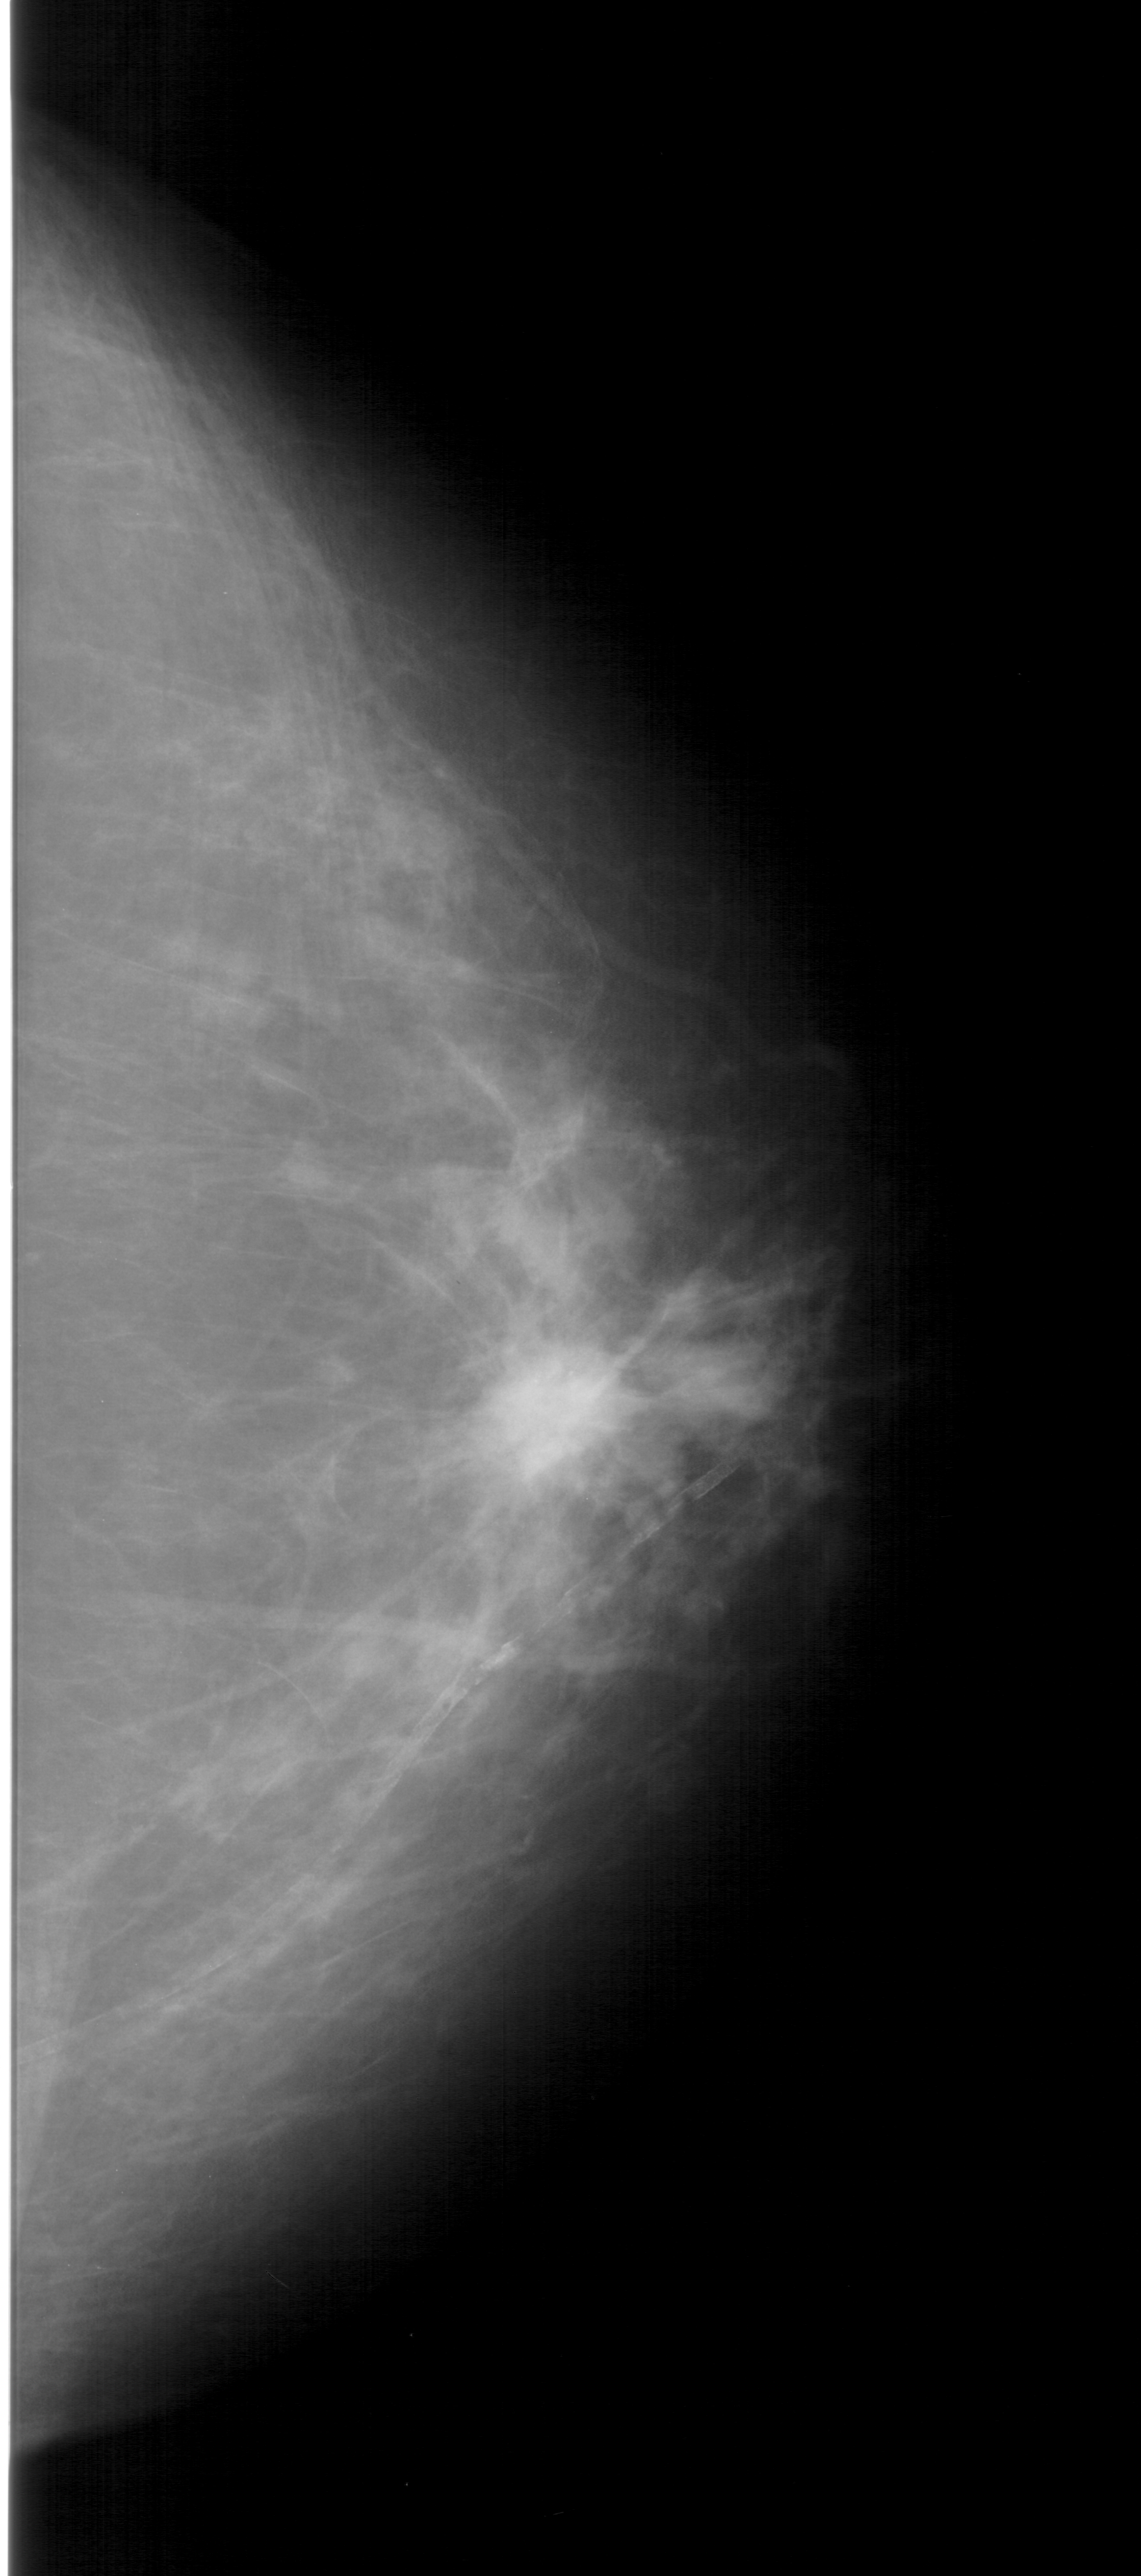
Mammogram (digitized film); right breast; craniocaudal (CC) view; 1141 × 2576 image matrix.
Marked abnormalities (boxes around the expert regions of interest):
- calcifications, morphology pleomorphic, distribution clustered; BI-RADS assessment category 5; subtlety rating 4 on a 1 (subtle) to 5 (obvious) scale; pathology result (as recorded, not read from the image): malignant: bounding box (x1, y1, x2, y2) in pixels: (329, 1170, 802, 1636)